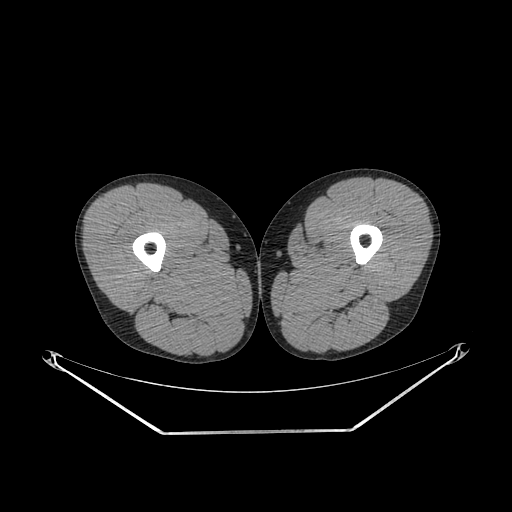
CT of an extremity soft-tissue mass (from a PET/CT study), one axial slice; position 264 of 311 along the scan axis; reconstruction kernel SOFT; 140 kVp; soft-tissue window (W 400 / L 40 HU); 512 × 512 image matrix. Male patient. Case-level facts recorded for this patient, not image findings: histological type: mixoid liposarcoma; grade: low; site of the primary tumour: left thigh.
Outlined on this slice (expert contour drawn on MRI and transferred to this co-registered scan by the dataset authors):
- gross tumour volume (mass): bounding box (x1, y1, x2, y2) in pixels: (304, 237, 321, 250)